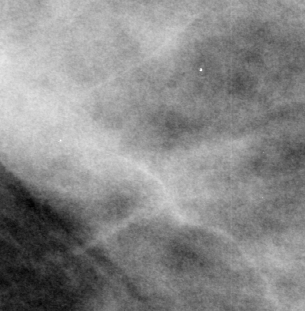
Crop from a digitized film mammogram around one marked abnormality, left breast, CC view.
Mass, shape oval, margins circumscribed; BI-RADS assessment category 3; subtlety rating 4 on a 1 (subtle) to 5 (obvious) scale; pathology result (as recorded, not read from the image): benign.